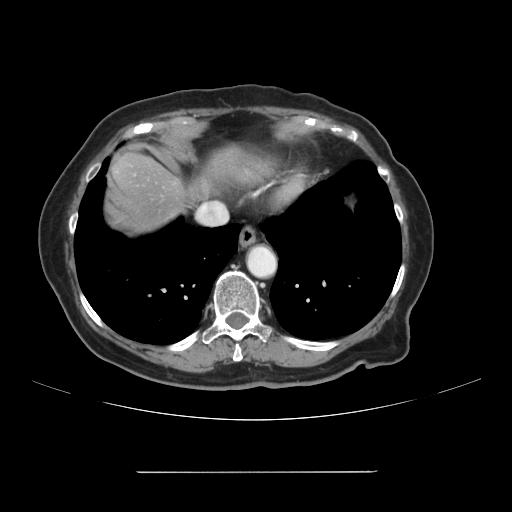
Contrast-enhanced abdominal CT, one axial slice. Position 101 of 111 along the scan axis. 120 kVp. Intravenous contrast given. Soft-tissue window (W 400 / L 40 HU). 2.5 mm slice thickness. 512 × 512 image matrix, field of view 400 × 400 mm. Female patient, age 74 years. From the clinical record (not read from this slice): diagnosis: colorectal cancer liver metastases, imaged before liver resection; multiple liver metastases: yes; largest metastasis: 1.1 cm.
Annotated regions visible in this slice (manually delineated by an expert):
- liver: bounding box (x1, y1, x2, y2) in pixels: (104, 145, 261, 236)
- planned liver remnant (the part of the liver to remain after resection): (208, 146, 262, 185)